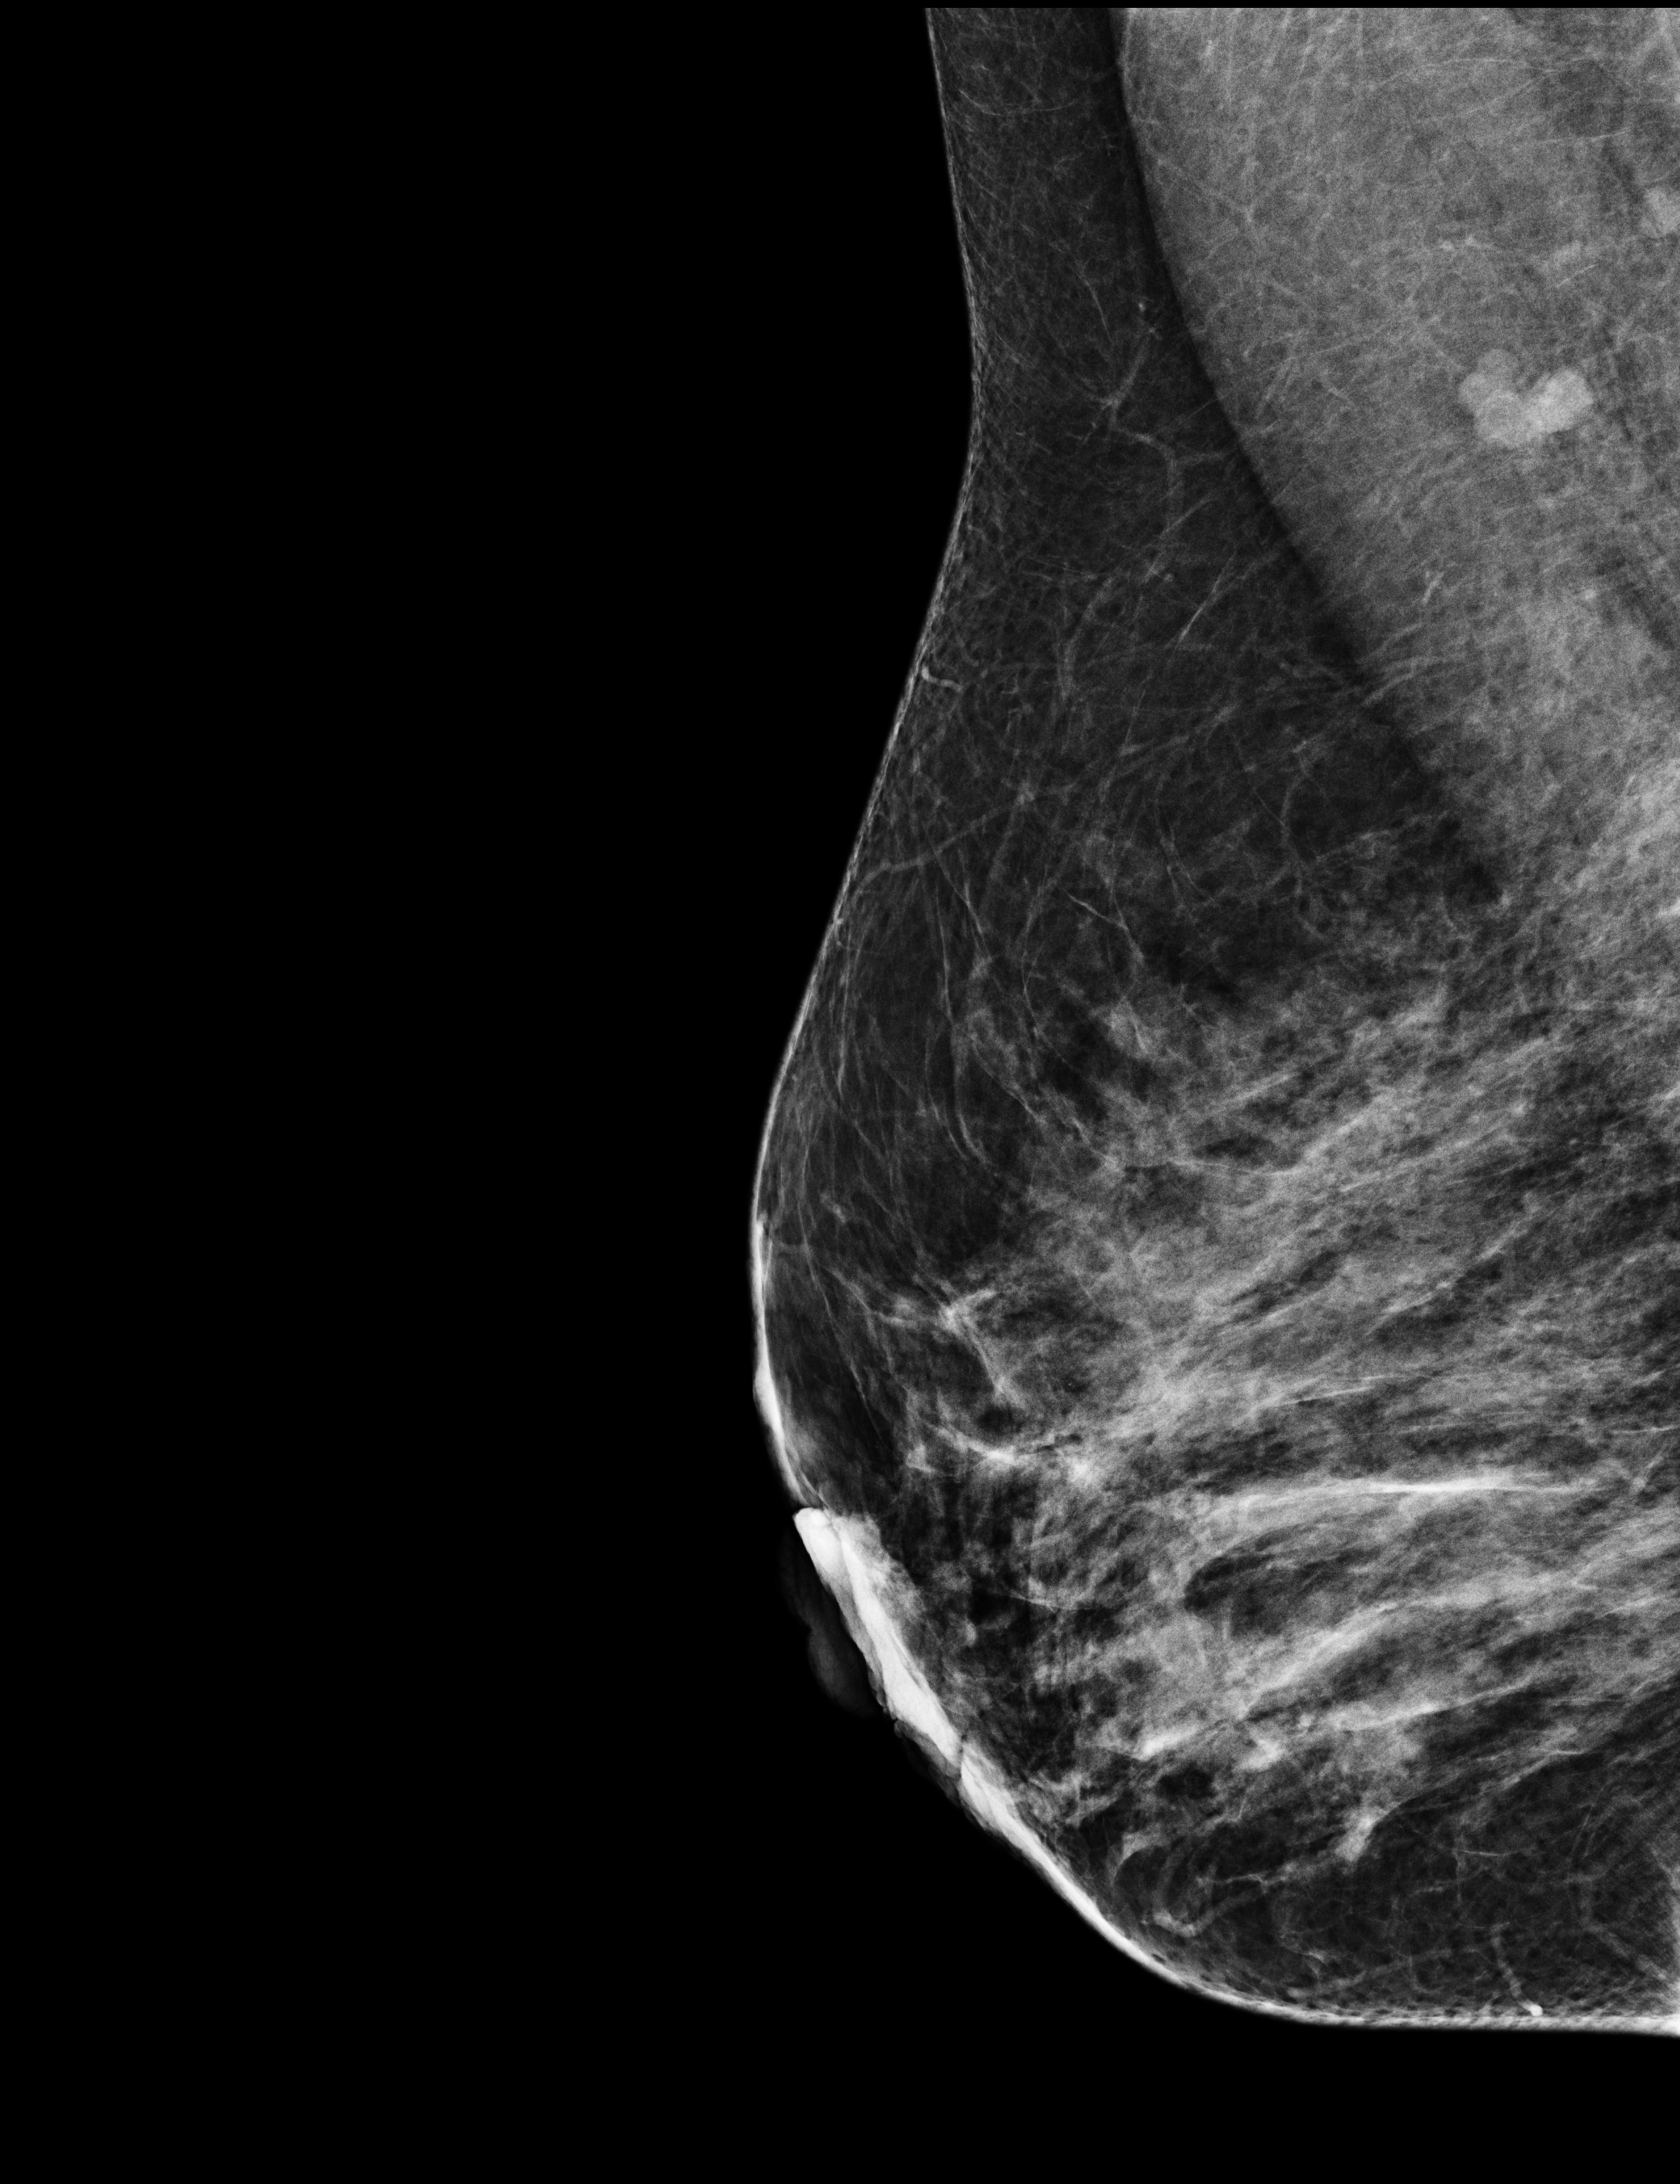
Full-field digital mammogram (FFDM); right breast; medio-lateral oblique projection; annual screening mammography examination; compressed breast thickness 58 mm; system: Selenia Dimensions. Female patient, age 42 years.
Breast density at the screening exam (both breasts): heterogeneously dense (BI-RADS density category c). Final BI-RADS assessment for this screening round (tomosynthesis exam, both breasts): category 1. Recall: no recall after this screen.